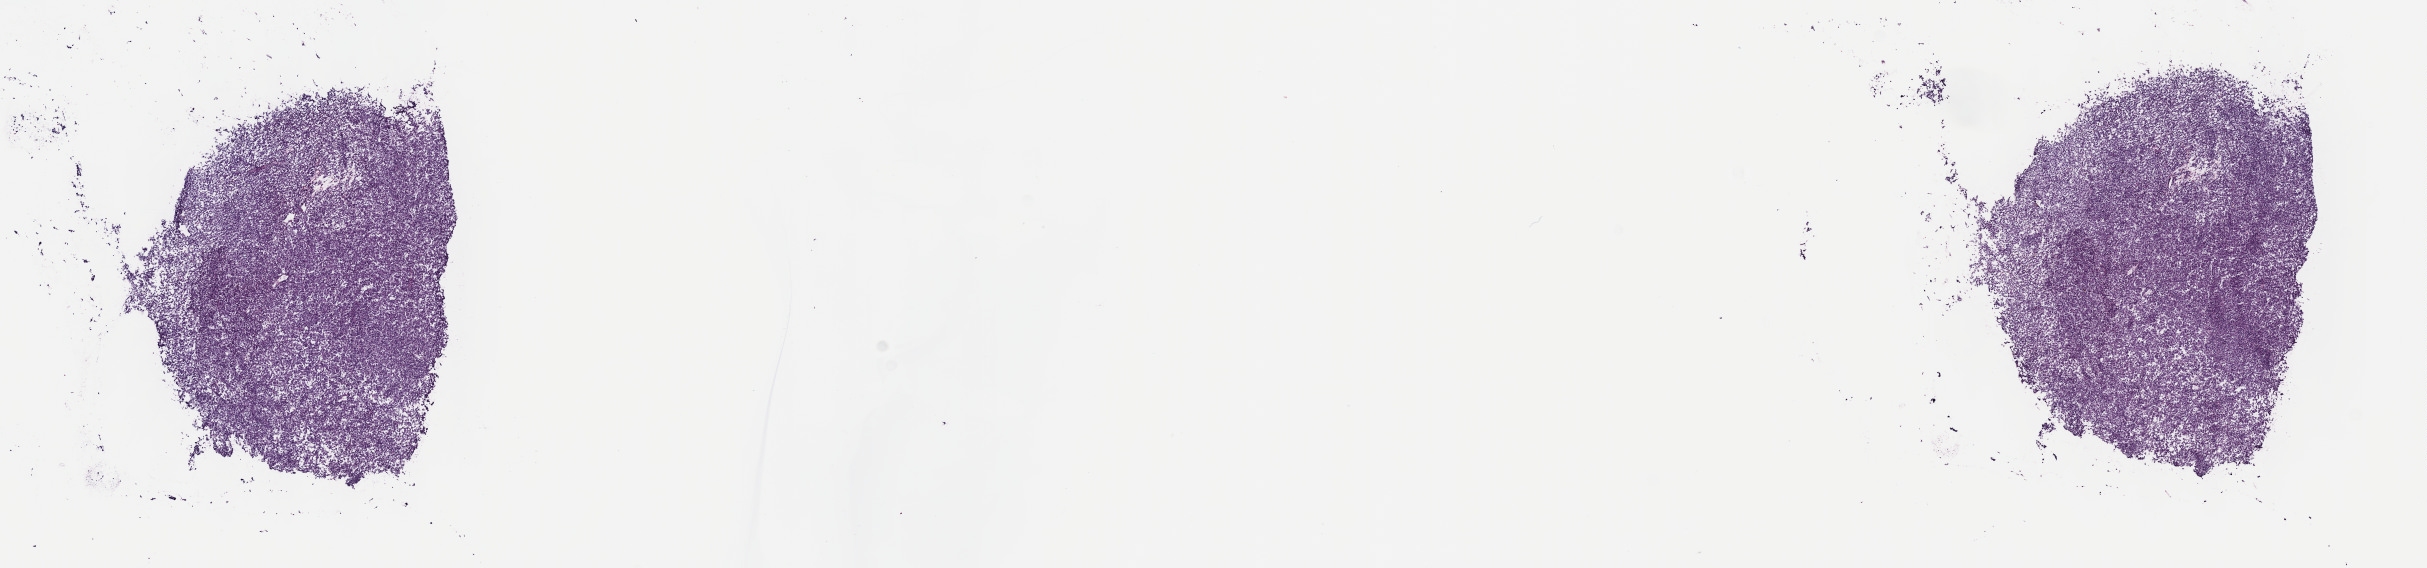
Digitized Hematoxylin and eosin (H&E) stained tissue section (whole slide) — shown as a low-resolution overview of the whole scanned area (about 19.6 x 4.6 mm), frozen section from the top of the tissue portion, uvea, primary tumour sample. Female patient; age at initial diagnosis 51 years. Composition of this section per pathologist review: tumour cells 100%, tumour nuclei 80%, normal cells 0%, stromal cells 0%, necrosis 0%. Infiltration values recorded for this section: lymphocyte infiltration 2%, monocyte infiltration 0%, neutrophil infiltration 0%.
AJCC pathologic stage: IIB. Pathologic diagnosis: Epithelioid cell melanoma (choroid).